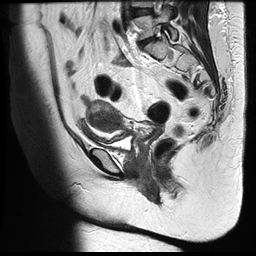
Pelvic MRI for cervical cancer, one sagittal slice. Slice 20 of 35 in the series (ordered by position). T2-weighted. 1.5 T. TE 122.8 ms, TR 4992 ms. 4 mm slice thickness. 256 × 256 image matrix. Female patient, age 42 years.
Annotated regions visible in this slice (expert manual segmentation):
- uterus and cervix: bounding box <86,100,125,133> (left, top, right, bottom; pixels)